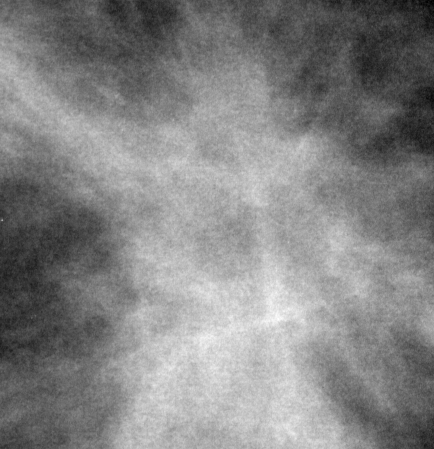
Region of interest cut from a scanned film mammogram (one marked finding); right breast; CC view; BI-RADS breast density category 2 (scale 1–4).
Mass, shape irregular, margins spiculated; BI-RADS assessment category 5; subtlety rating 5 on a 1 (subtle) to 5 (obvious) scale; pathology (as recorded): malignant.